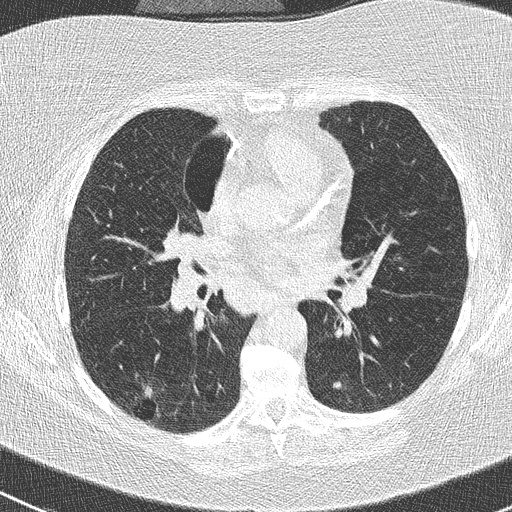
Low-dose screening chest CT, axial slice. Baseline annual screen. Lung window (W 1500 / L -600 HU). 2 mm slice thickness. 512 × 512 image matrix, field of view 310 × 310 mm. Female, age 74 years at enrolment. Former smoker at enrolment.
Expert reader's lesion annotation, bounding box <121,372,175,432> (left, top, right, bottom; pixels). The screening reader recorded 3 non-calcified nodules or masses ≥4 mm on this exam (right lower lobe, right upper lobe, left lower lobe); which of them this box marks is not recorded. Official screen result: positive, change unspecified: nodule(s) >= 4 mm or enlarging nodule(s), mass(es), or other non-specific abnormalities suspicious for lung cancer. Later outcome: lung cancer diagnosed 16 days after this screen — non-small cell carcinoma, right lower lobe, poorly differentiated (G3), stage IIIA (AJCC 6th edition), 28 mm at pathology.